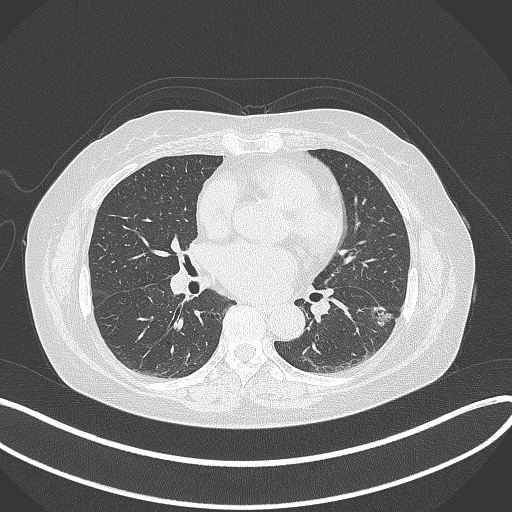
Chest CT, one axial slice. Position 175 of 373 along the scan axis. 120 kVp. Lung window (W 1500 / L -600 HU). 1 mm slice thickness. 512 × 512 image matrix, field of view 400 × 400 mm. Patient: female, 67 years. Case-level facts recorded for this patient, not image findings: clinical TNM (as recorded): T1c N0 M0.
Structures marked on this image (bounding box drawn by a radiologist):
- lung tumour (recorded histology: adenocarcinoma): bounding box <361,299,398,332> (left, top, right, bottom; pixels)